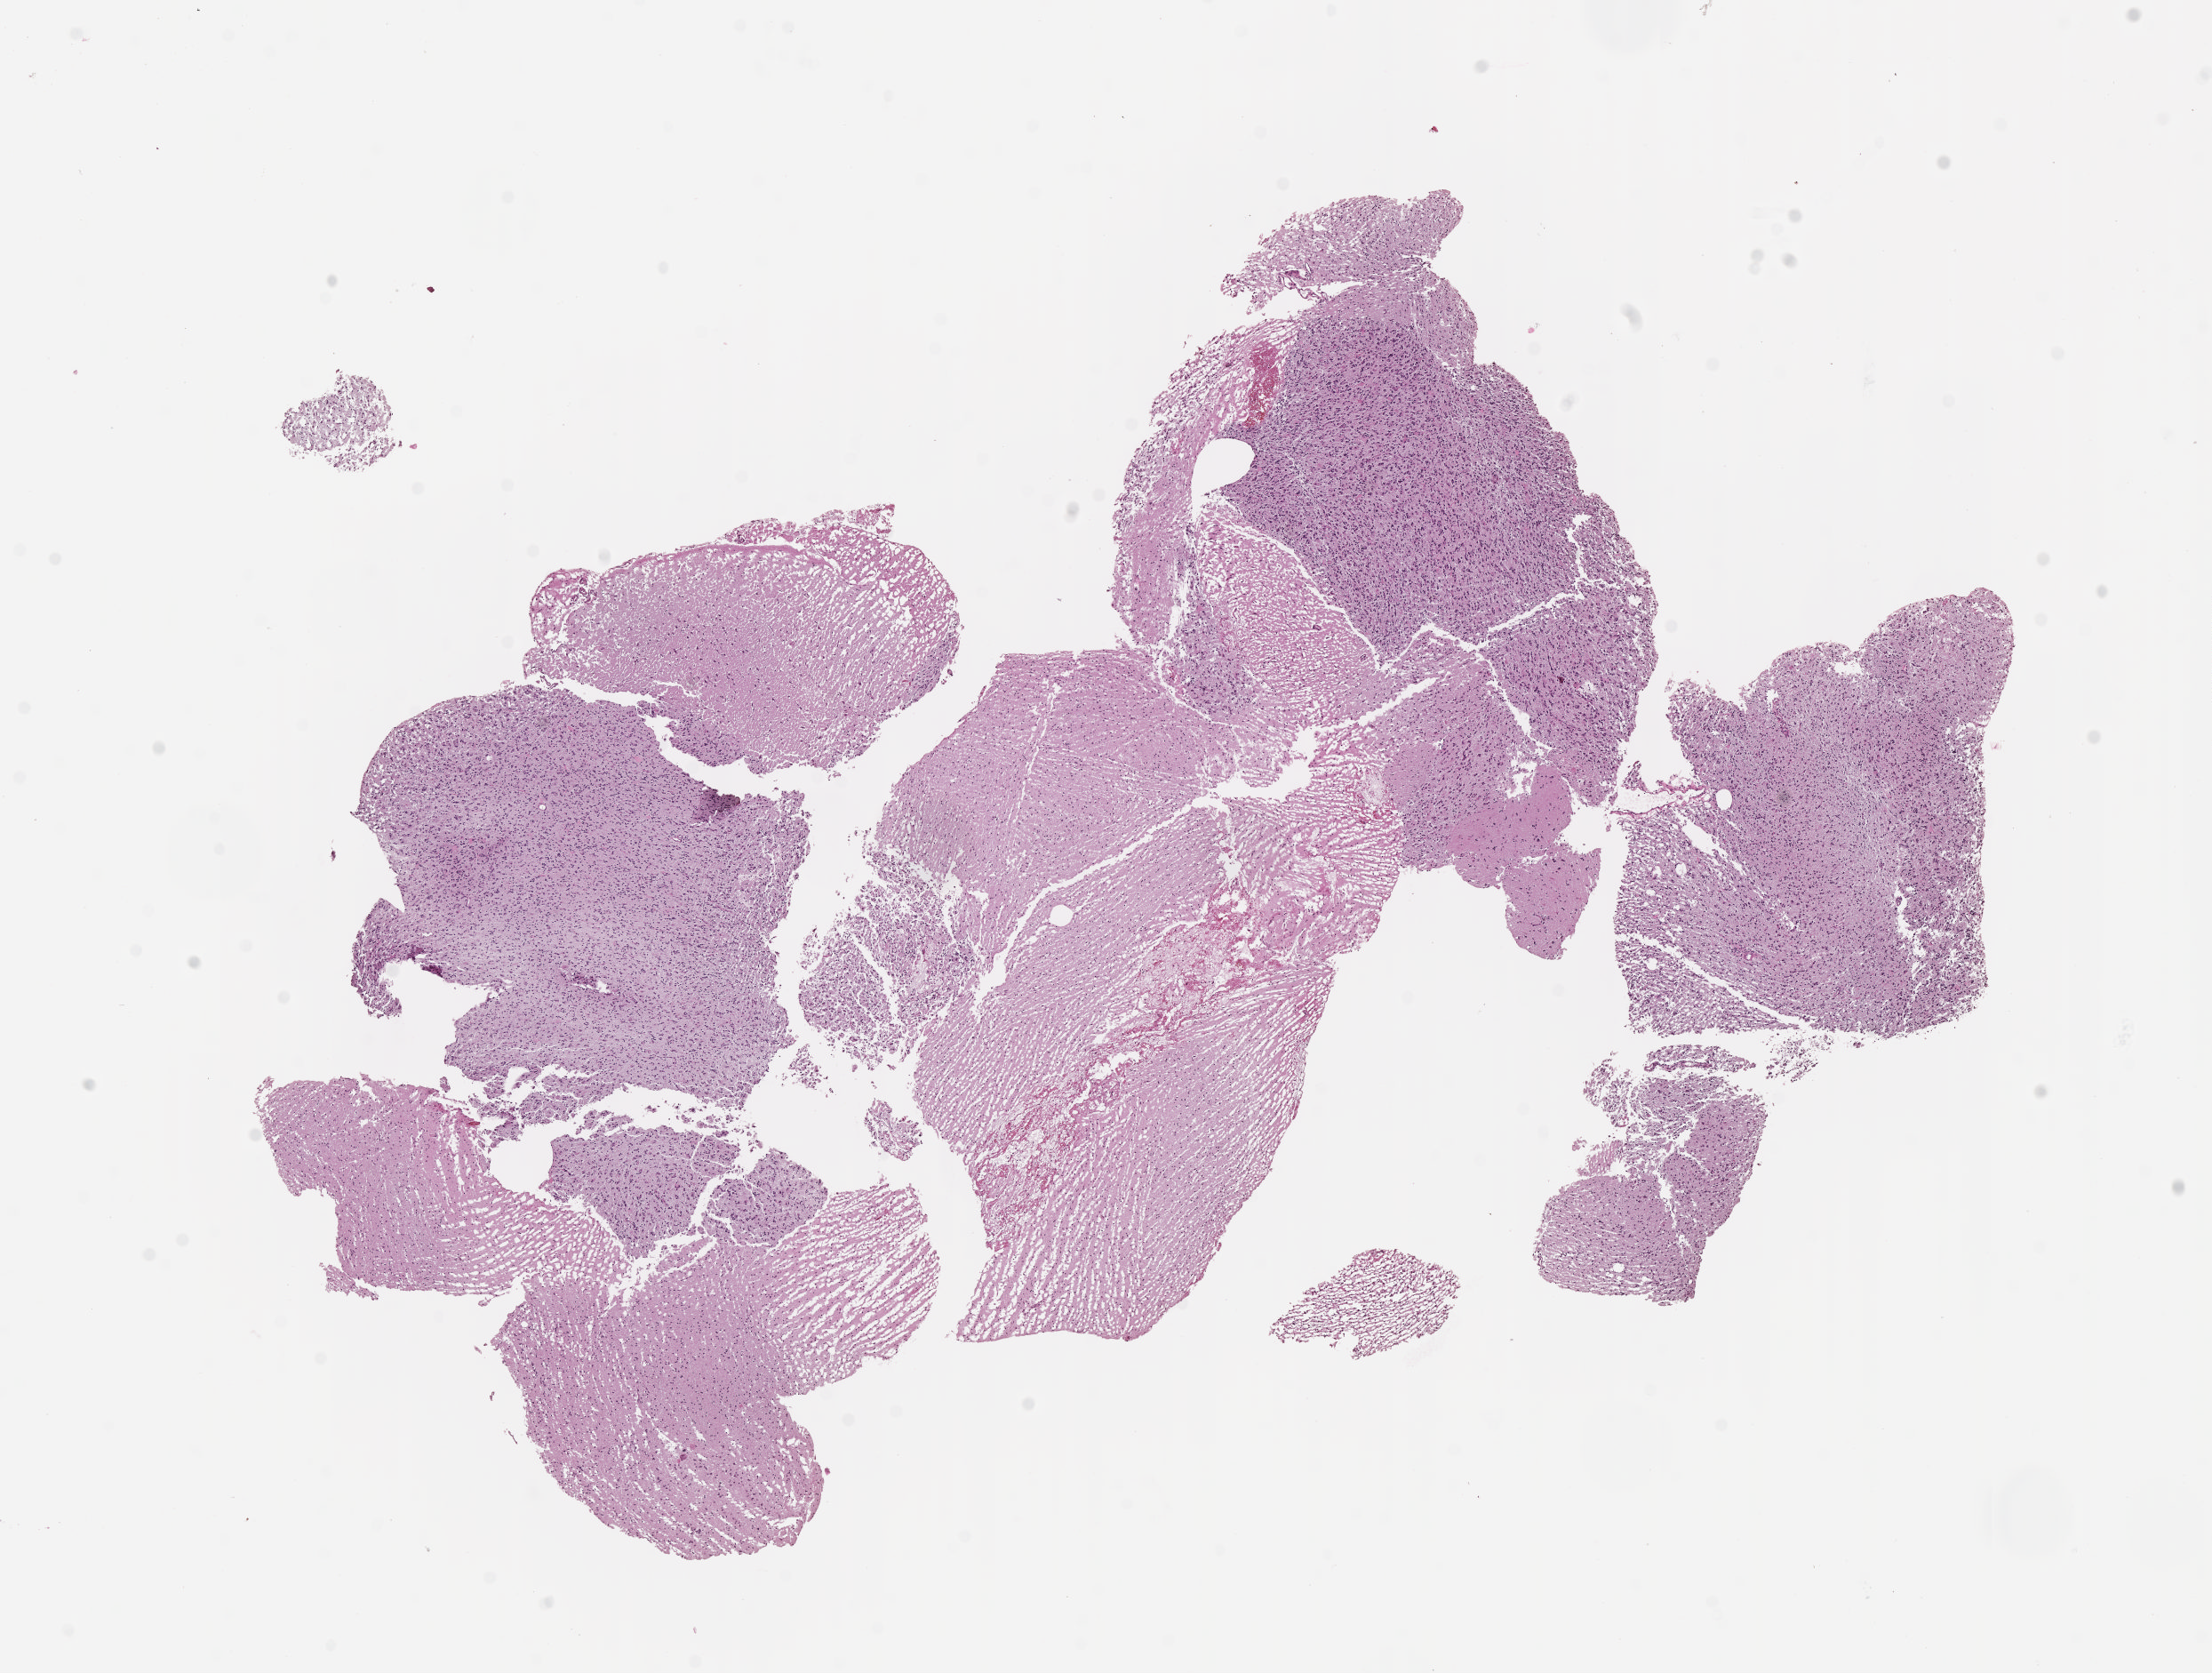
Digitized H&E-stained tissue section (whole slide) — whole scanned area (about 10.1 x 7.6 mm) shown as a low-resolution overview, FFPE section, sample: primary tumour, brain. Male patient; age at initial diagnosis 56 years.
Pathologic diagnosis: Oligodendroglioma, NOS (cerebrum).